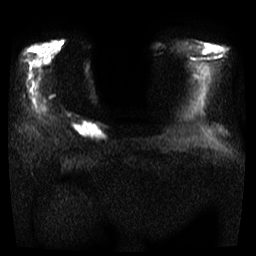
Breast MRI, one axial slice. Slice 8 of 35 in the series (ordered by position). Diffusion-weighted series; image 2 of 4 stored at this slice position (different b-values; order by instance number). 3 T. 5 mm slice thickness. 256 × 256 image matrix, field of view 300 × 300 mm. Female patient.
Outlined on this slice (expert manual segmentation):
- tumour on diffusion-weighted imaging: bounding box [x1, y1, x2, y2] px = [73, 120, 107, 140]